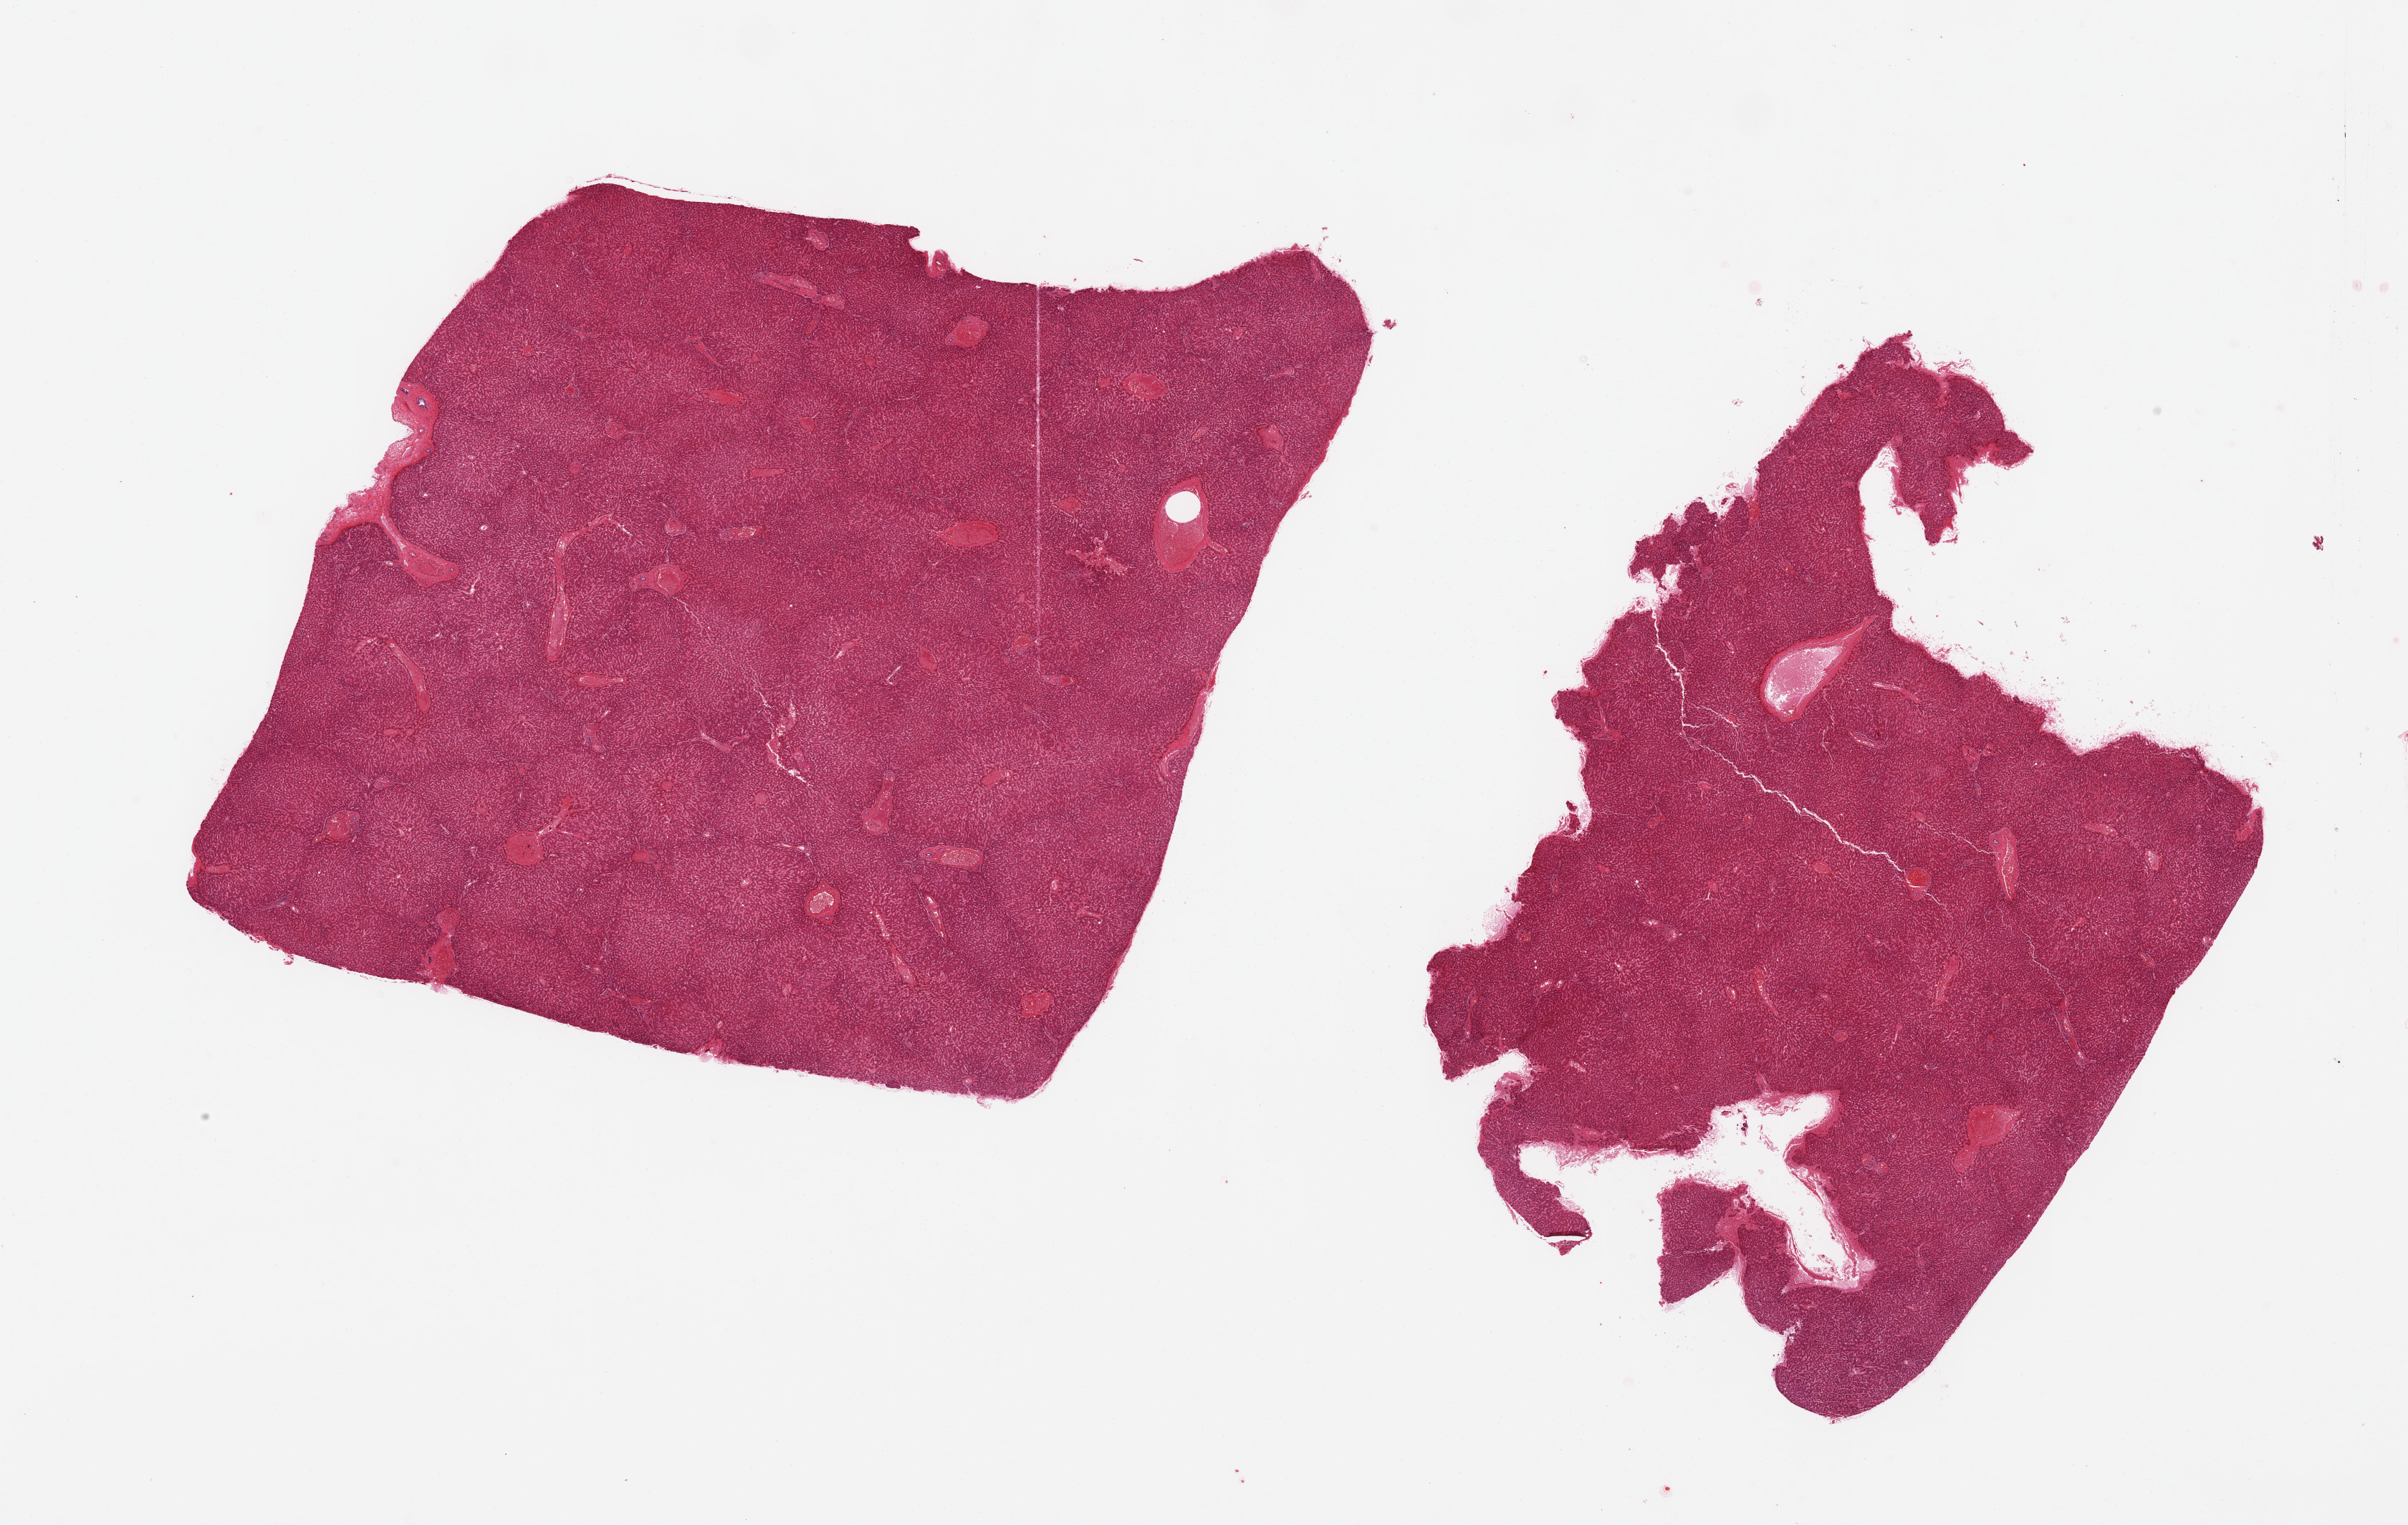
H&E whole-slide image, whole scanned area (about 26.6 x 16.8 mm) shown as a low-resolution overview. PAXgene-fixed, paraffin-embedded tissue. Target tissue: liver. Donor tissue sample.
- pathologist's review note for this sample: 2 pieces; central vein congestion